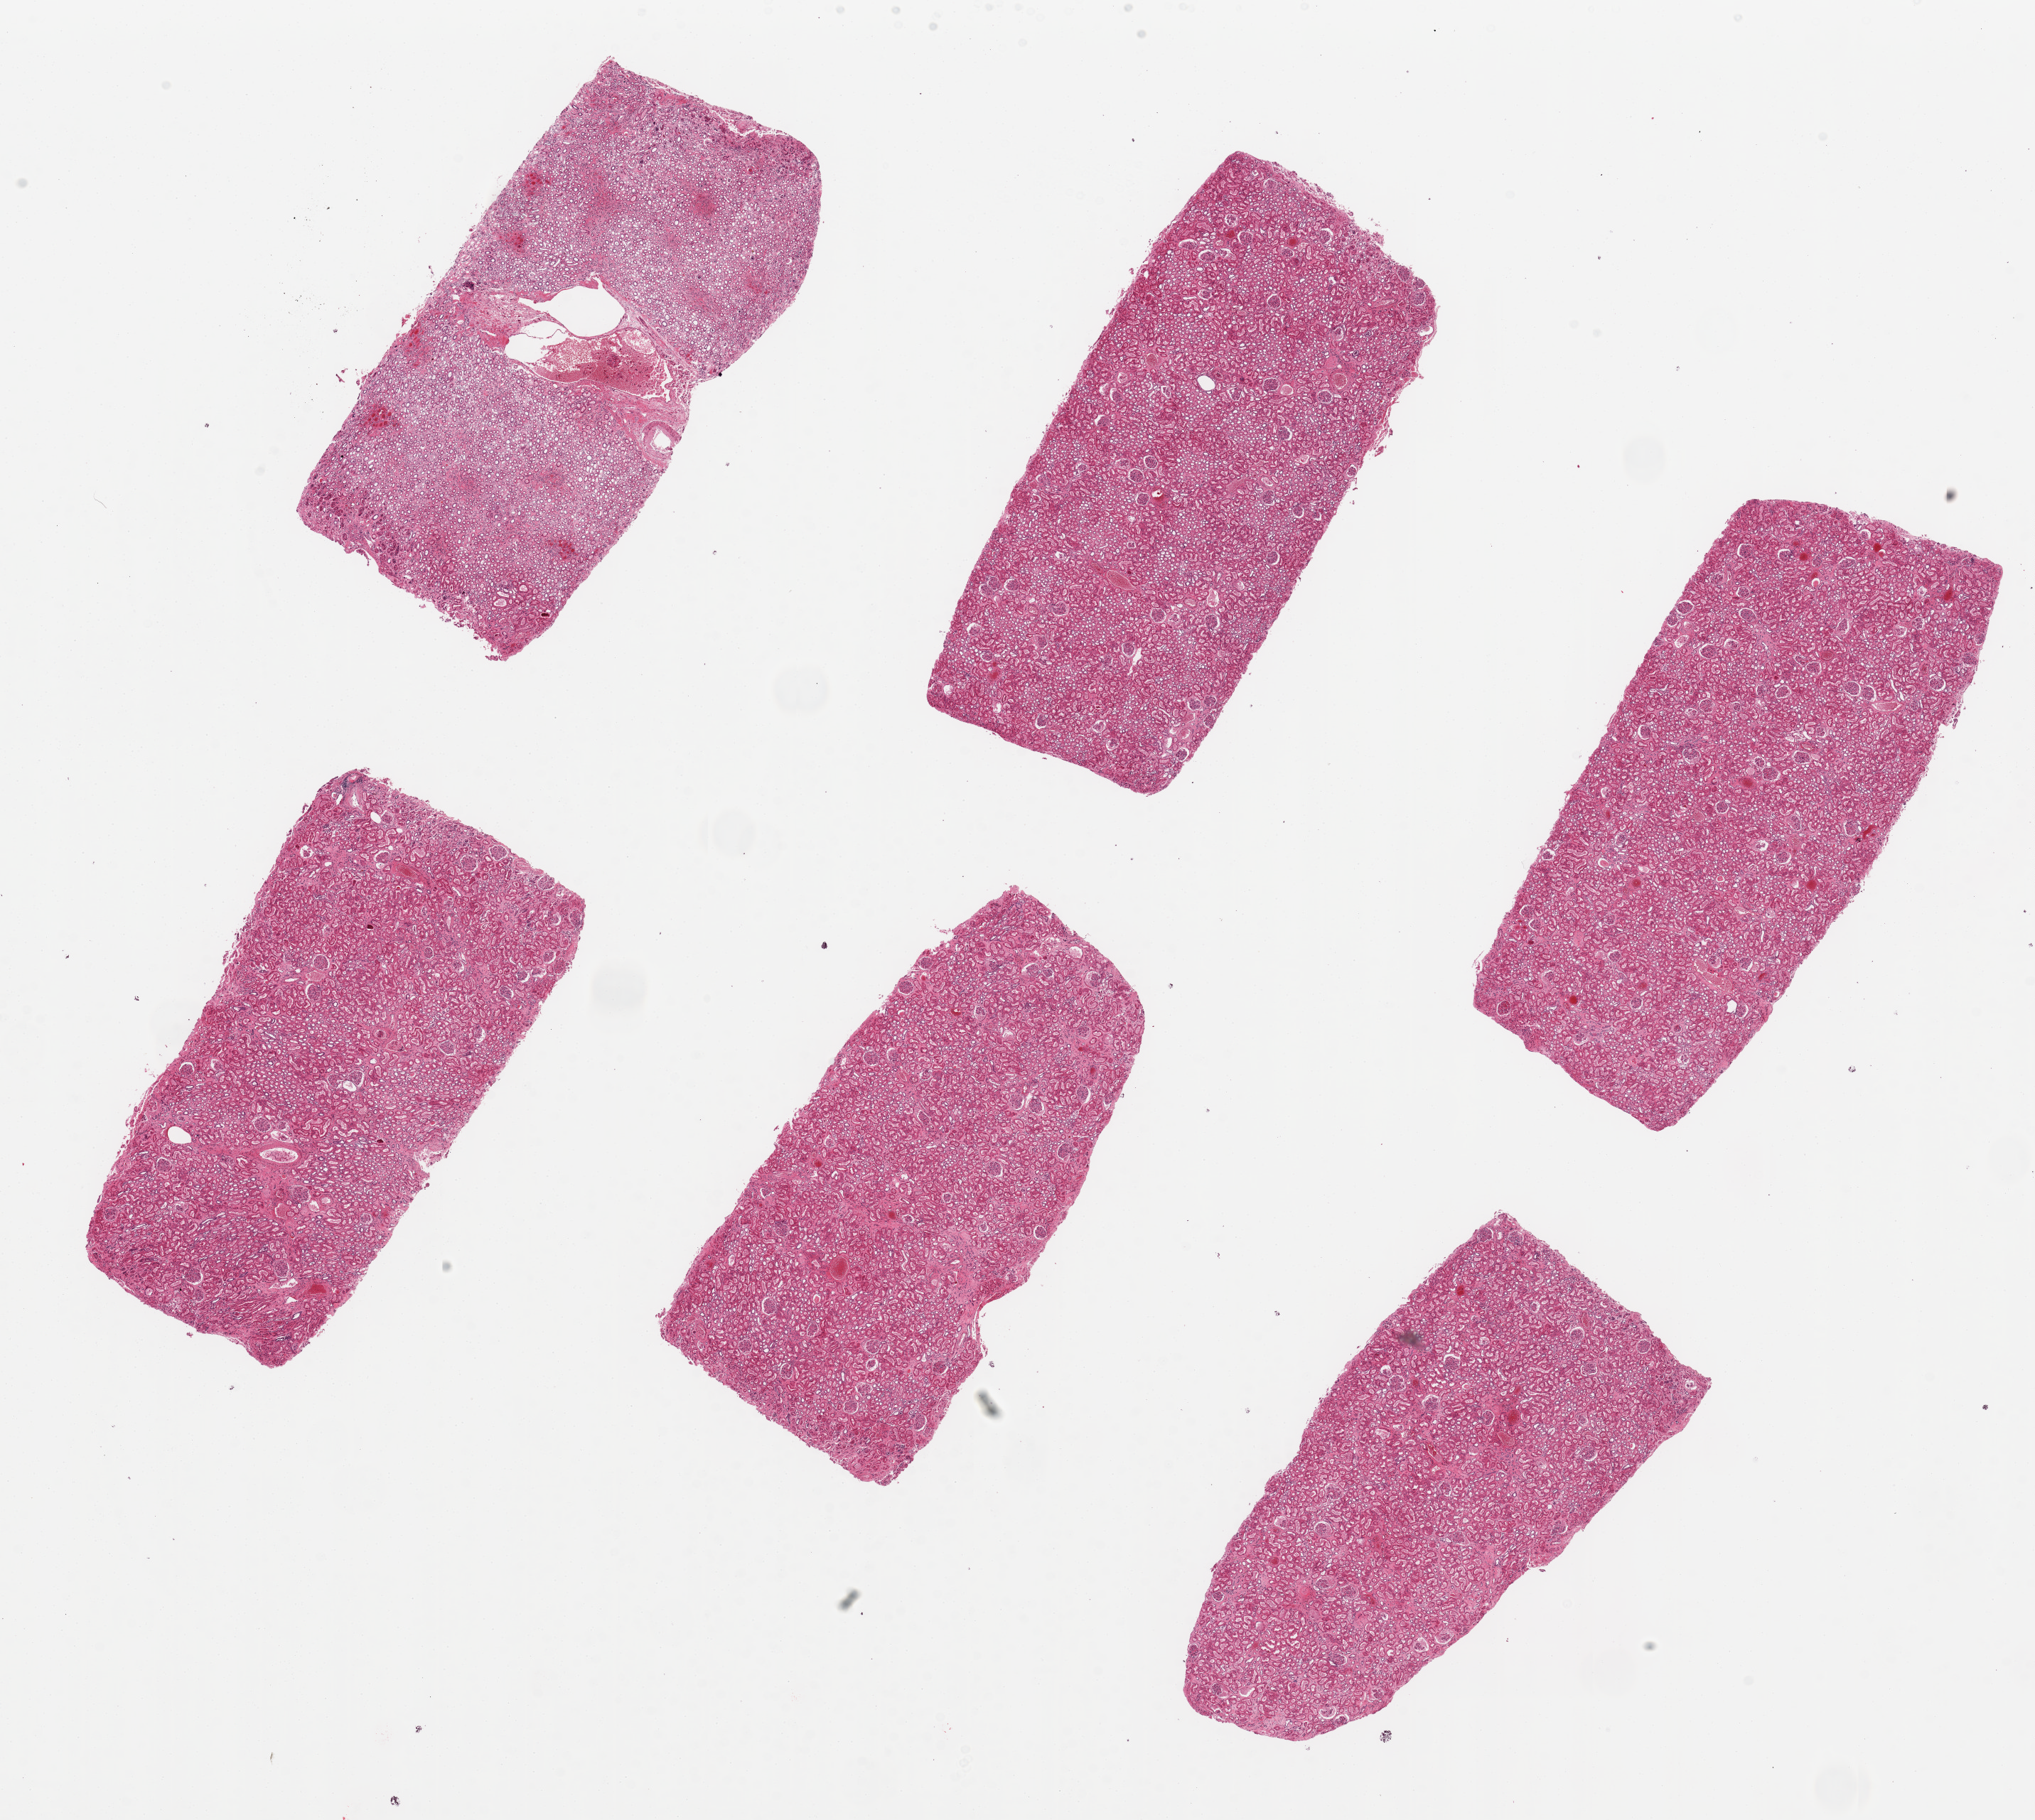
Digitized haematoxylin and eosin-stained section, shown as a low-resolution overview of the whole scanned area (about 22.6 x 20.3 mm, from a 20x scan); PAXgene-fixed, paraffin-embedded tissue; section of renal cortex (target tissue); tissue donor sample. Male donor.
Review note (as recorded): 6 pieces, up to 7x3 mm; 5 are cortex, 1 is medulla.